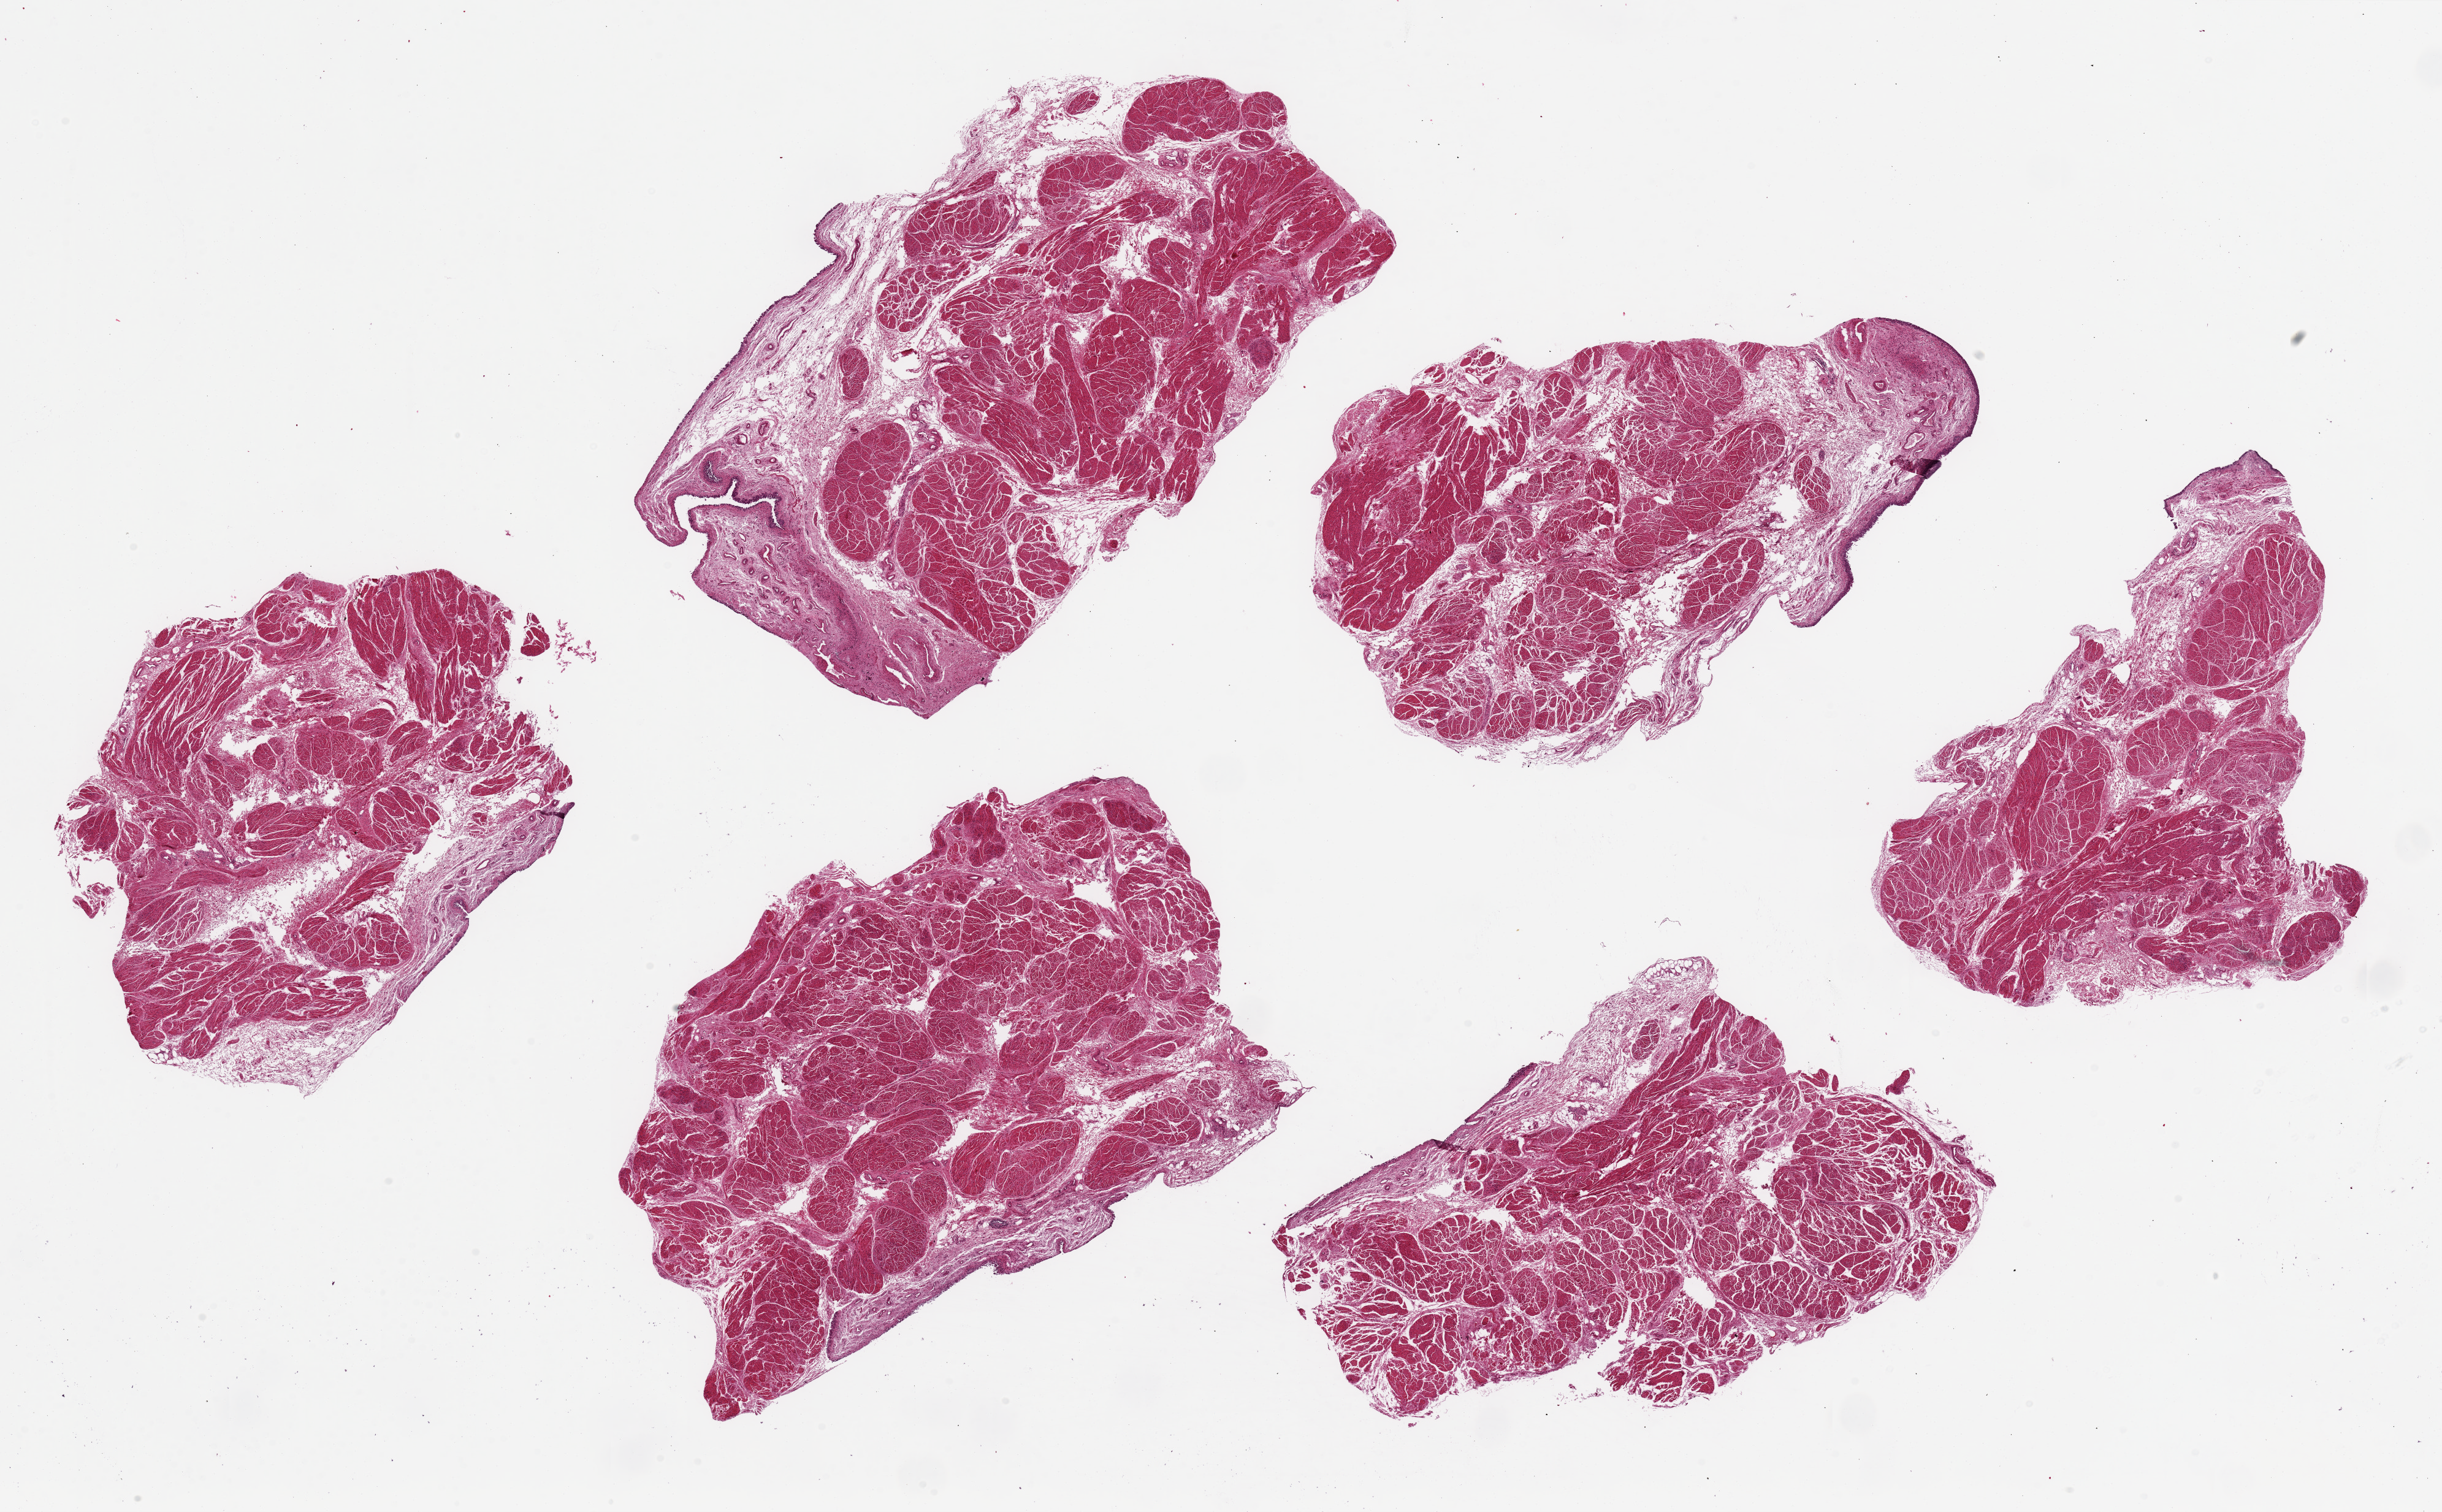
Digitized haematoxylin and eosin-stained section, shown as a low-resolution overview of the whole scanned area (about 31.5 x 19.5 mm, from a 20x scan). PAXgene-fixed paraffin-embedded (PFPE) section. Sampled site (target tissue): urinary bladder. Donor tissue sample.
Pathologist's review note for this sample: 6 pieces up to 9x5 mm; surface mostly sloughed.